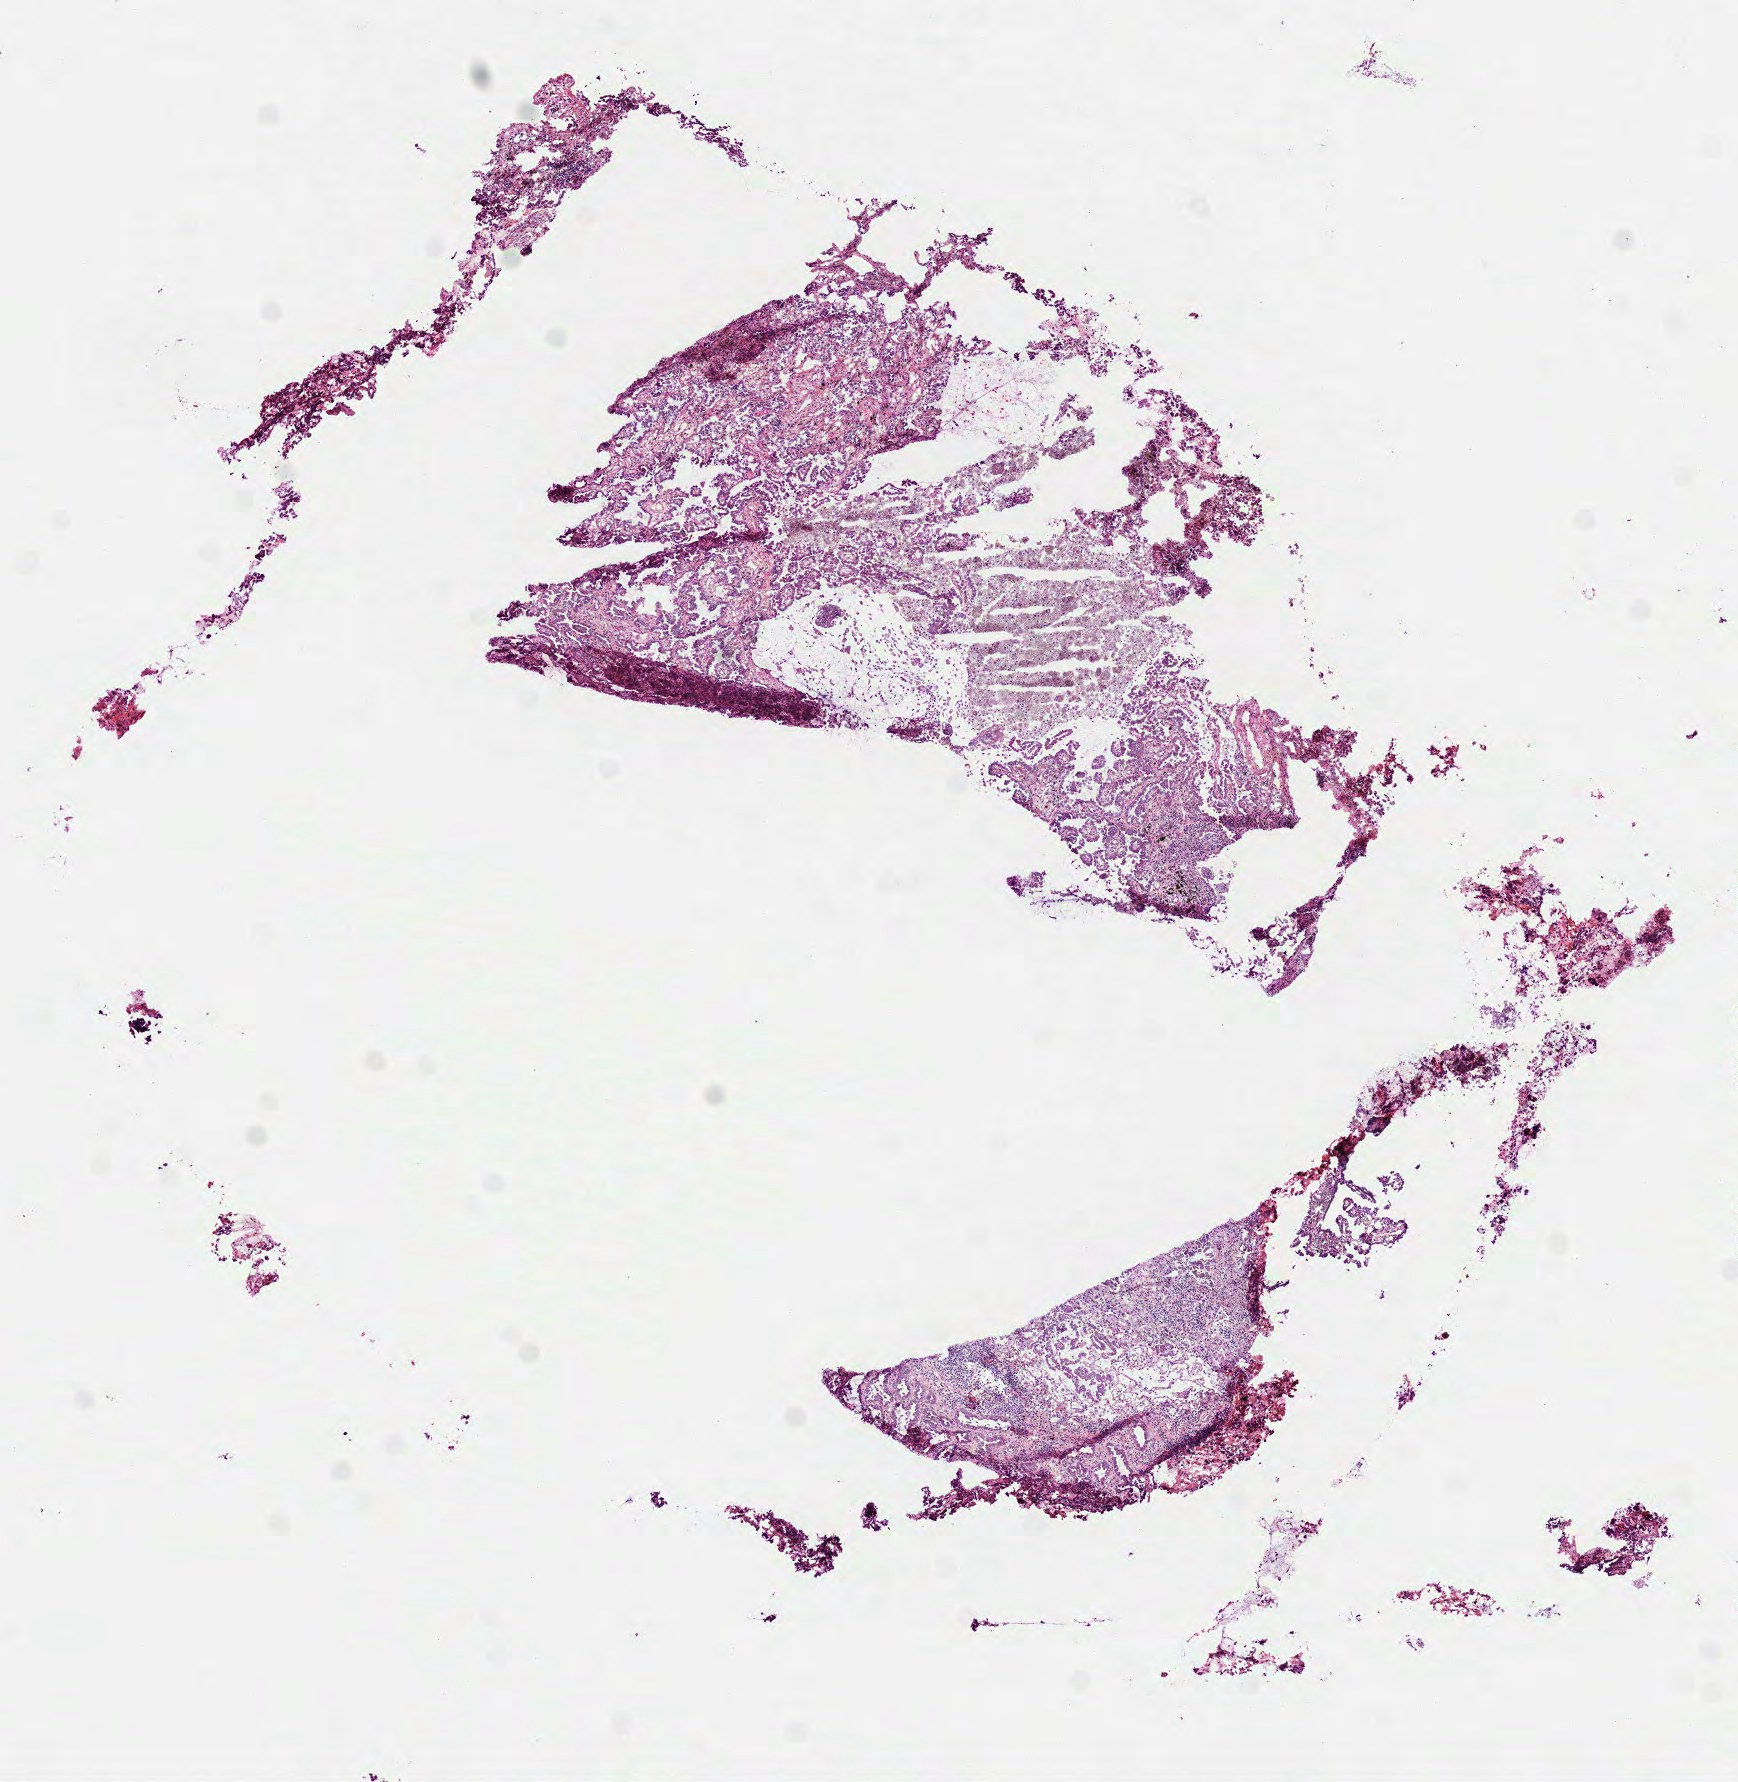
Whole-slide histology image, H&E-stained — low-resolution overview of the scanned area, about 7.0 x 7.2 mm (from a 40x scan); frozen section from the bottom of the tissue portion; sample: primary tumour, lung. Patient: male, age at initial diagnosis 65 years. Pathologist review of this section (percent, as recorded): tumour cells 70%, tumour nuclei 70%.
Pathologic diagnosis: Adenocarcinoma with mixed subtypes (upper lobe, lung).